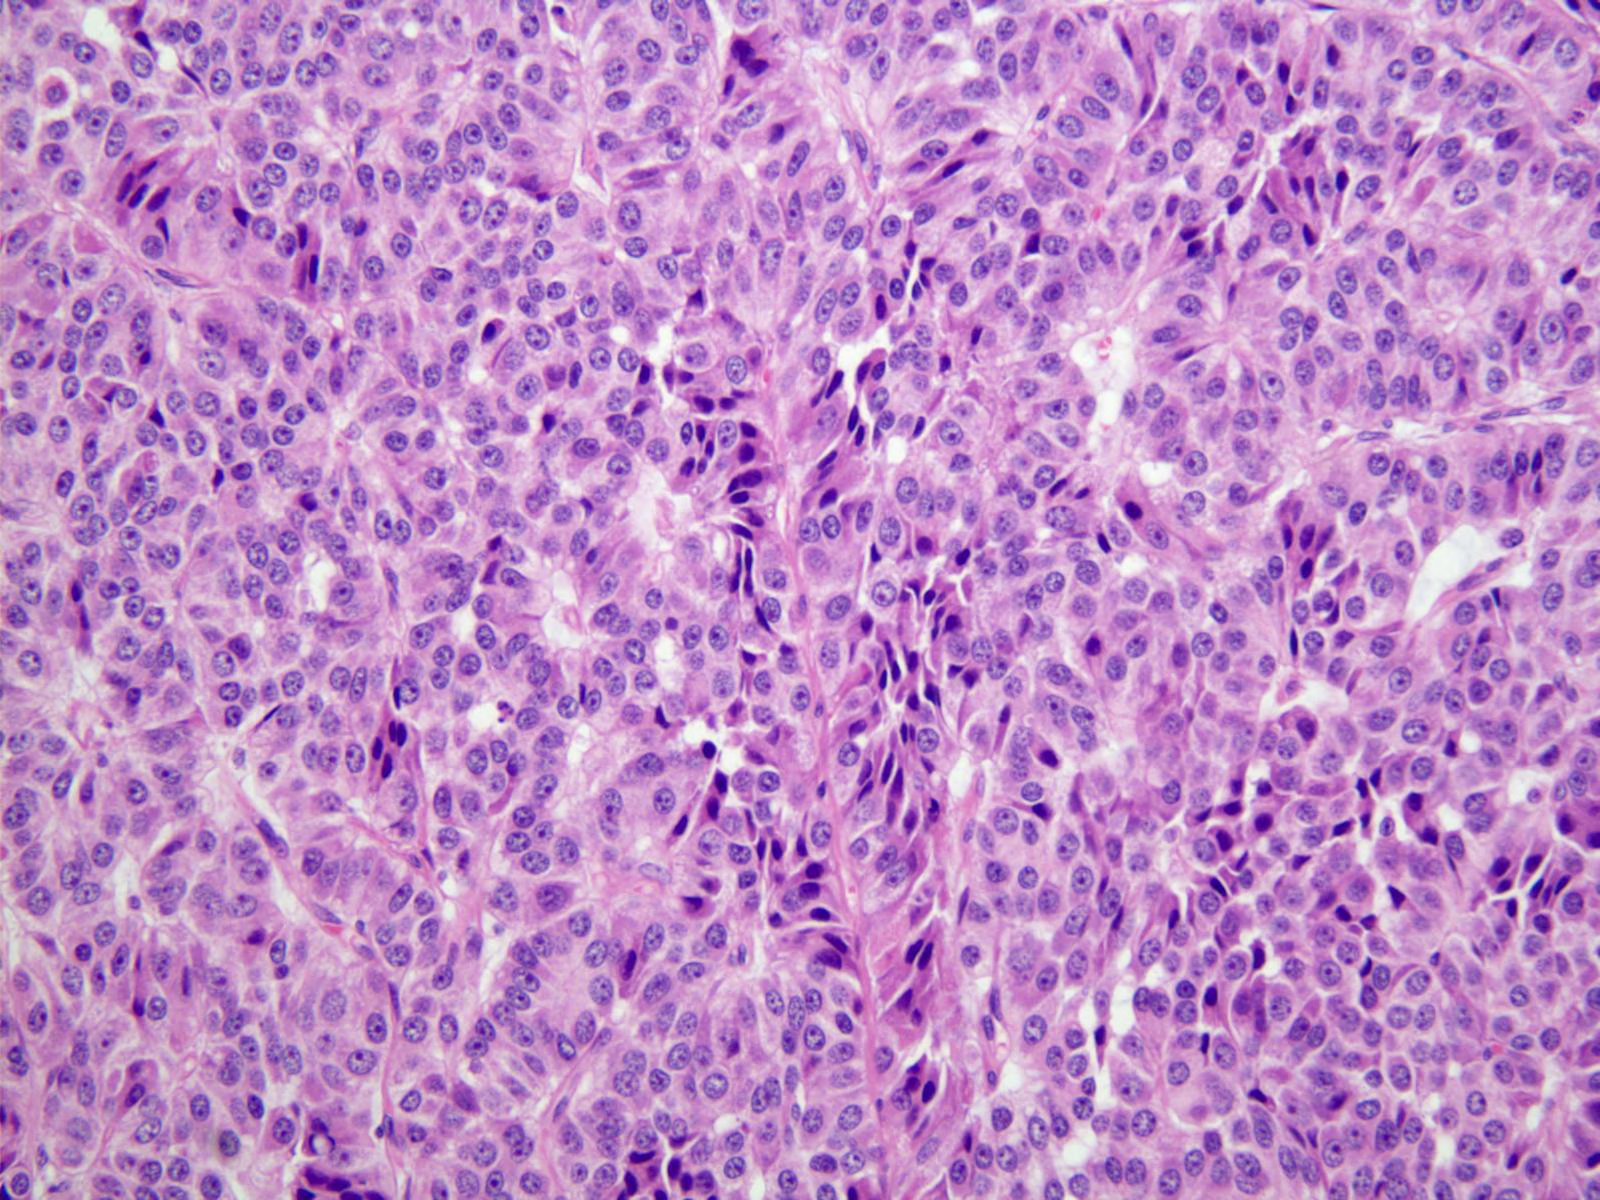
Single-field H&E photomicrograph — roughly 0.8 x 0.6 mm in extent. Formalin-fixed paraffin-embedded (FFPE) diagnostic section. Sample: primary tumour, stomach. Male patient; age at initial diagnosis 65 years. Histologic grade: G2 (moderately differentiated).
- pathologic diagnosis: Tubular adenocarcinoma